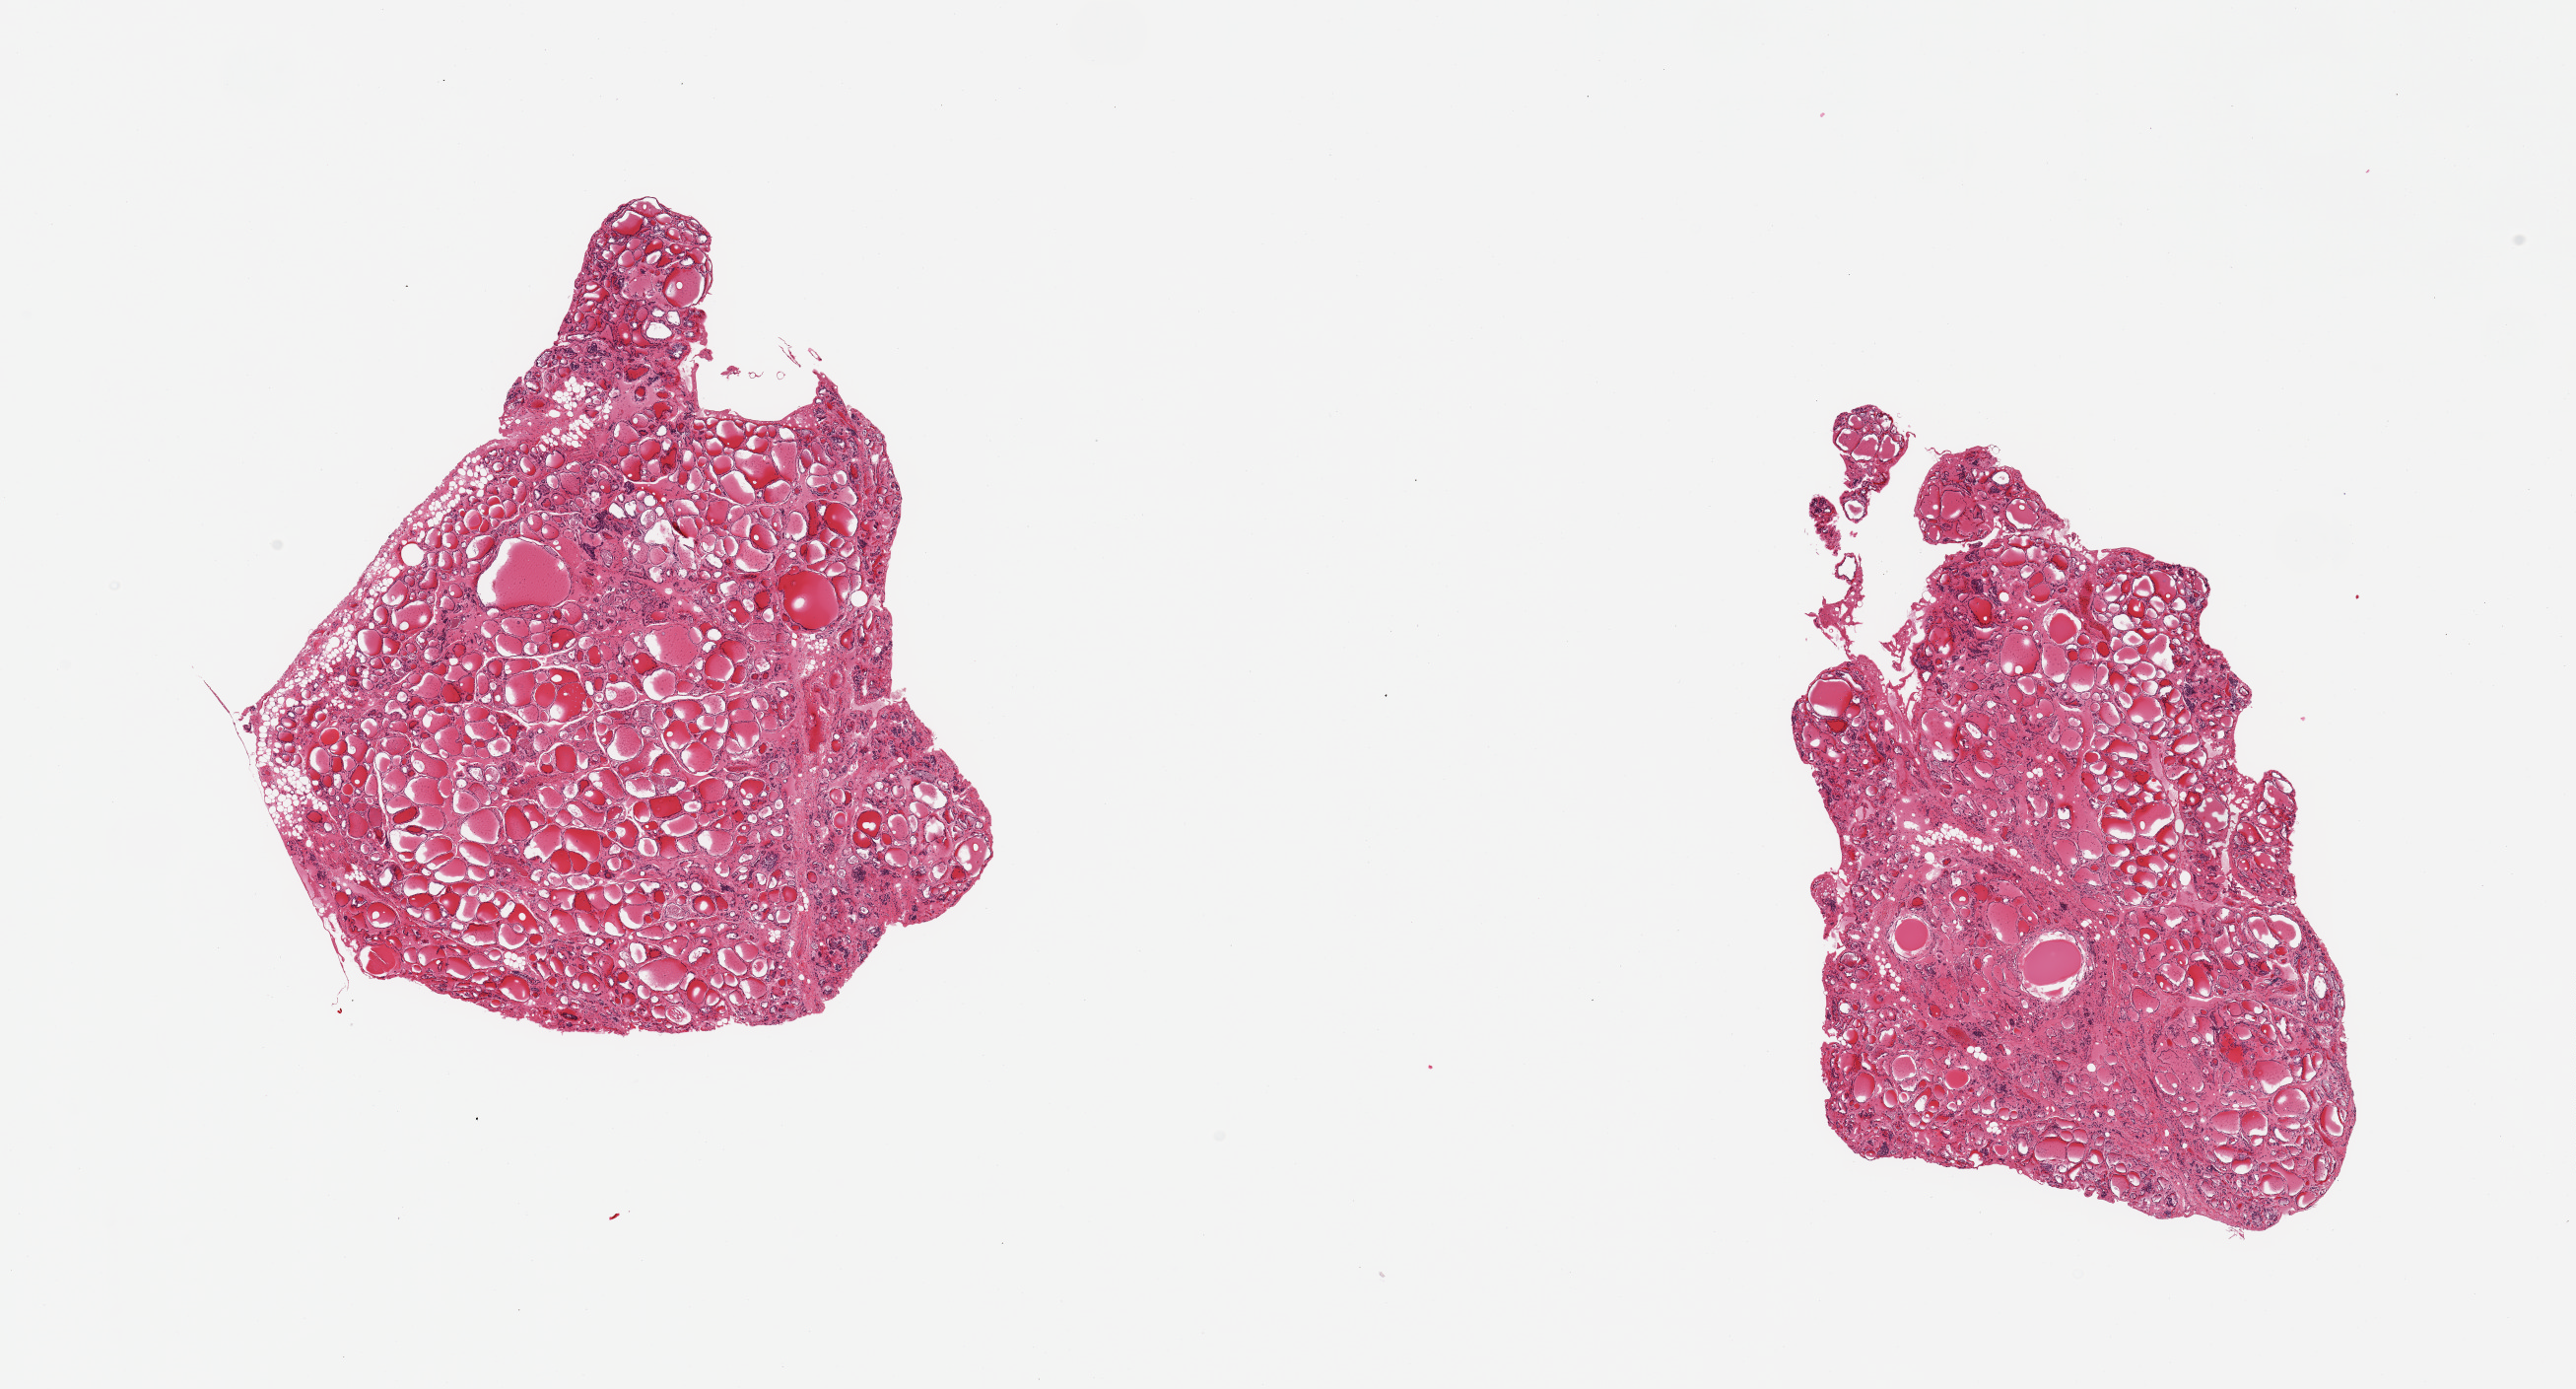
H&E whole-slide image, a low-resolution overview of the entire scanned area, about 20.7 x 11.1 mm (slide scanned at 20x). PAXgene-fixed paraffin-embedded (PFPE) section. Sampled site (target tissue): thyroid. Tissue donor sample.
* review note (as recorded): 2 pieces; well dissected